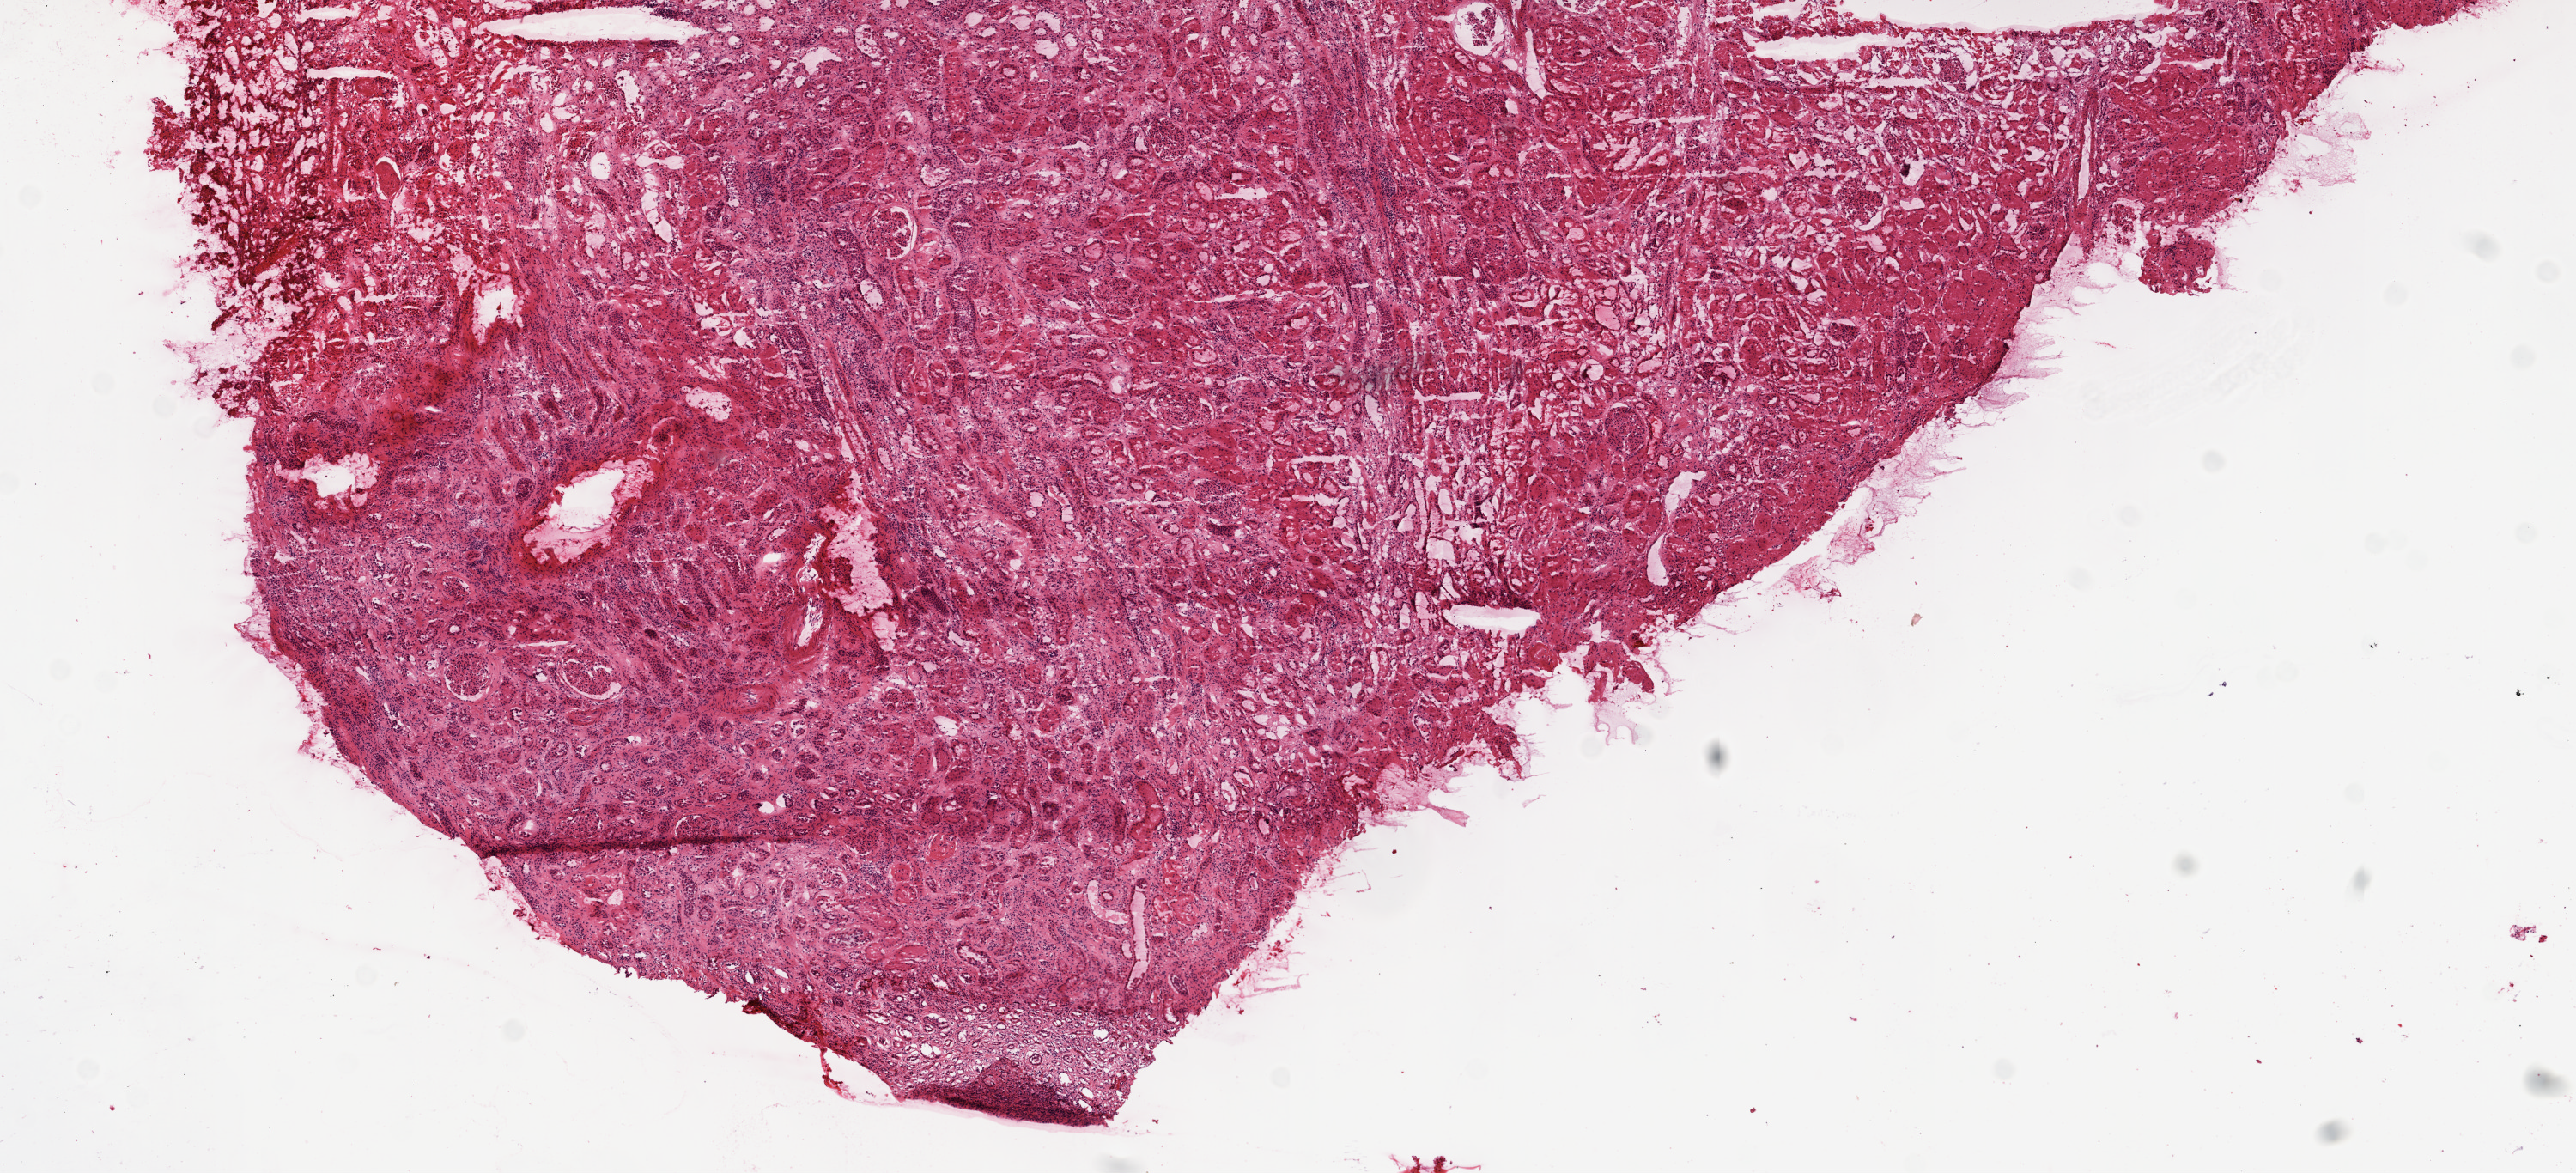
Digitized H&E tissue section (whole slide) — a low-resolution overview of the entire scanned area, about 12.0 x 5.5 mm; frozen section from the top of the tissue portion; kidney, solid tissue normal (non-tumour tissue) sample. Patient: female, age at initial diagnosis 77 years.
• this section: solid tissue normal (non-tumour) sample from the same patient
• patient diagnosis: Clear cell adenocarcinoma, NOS